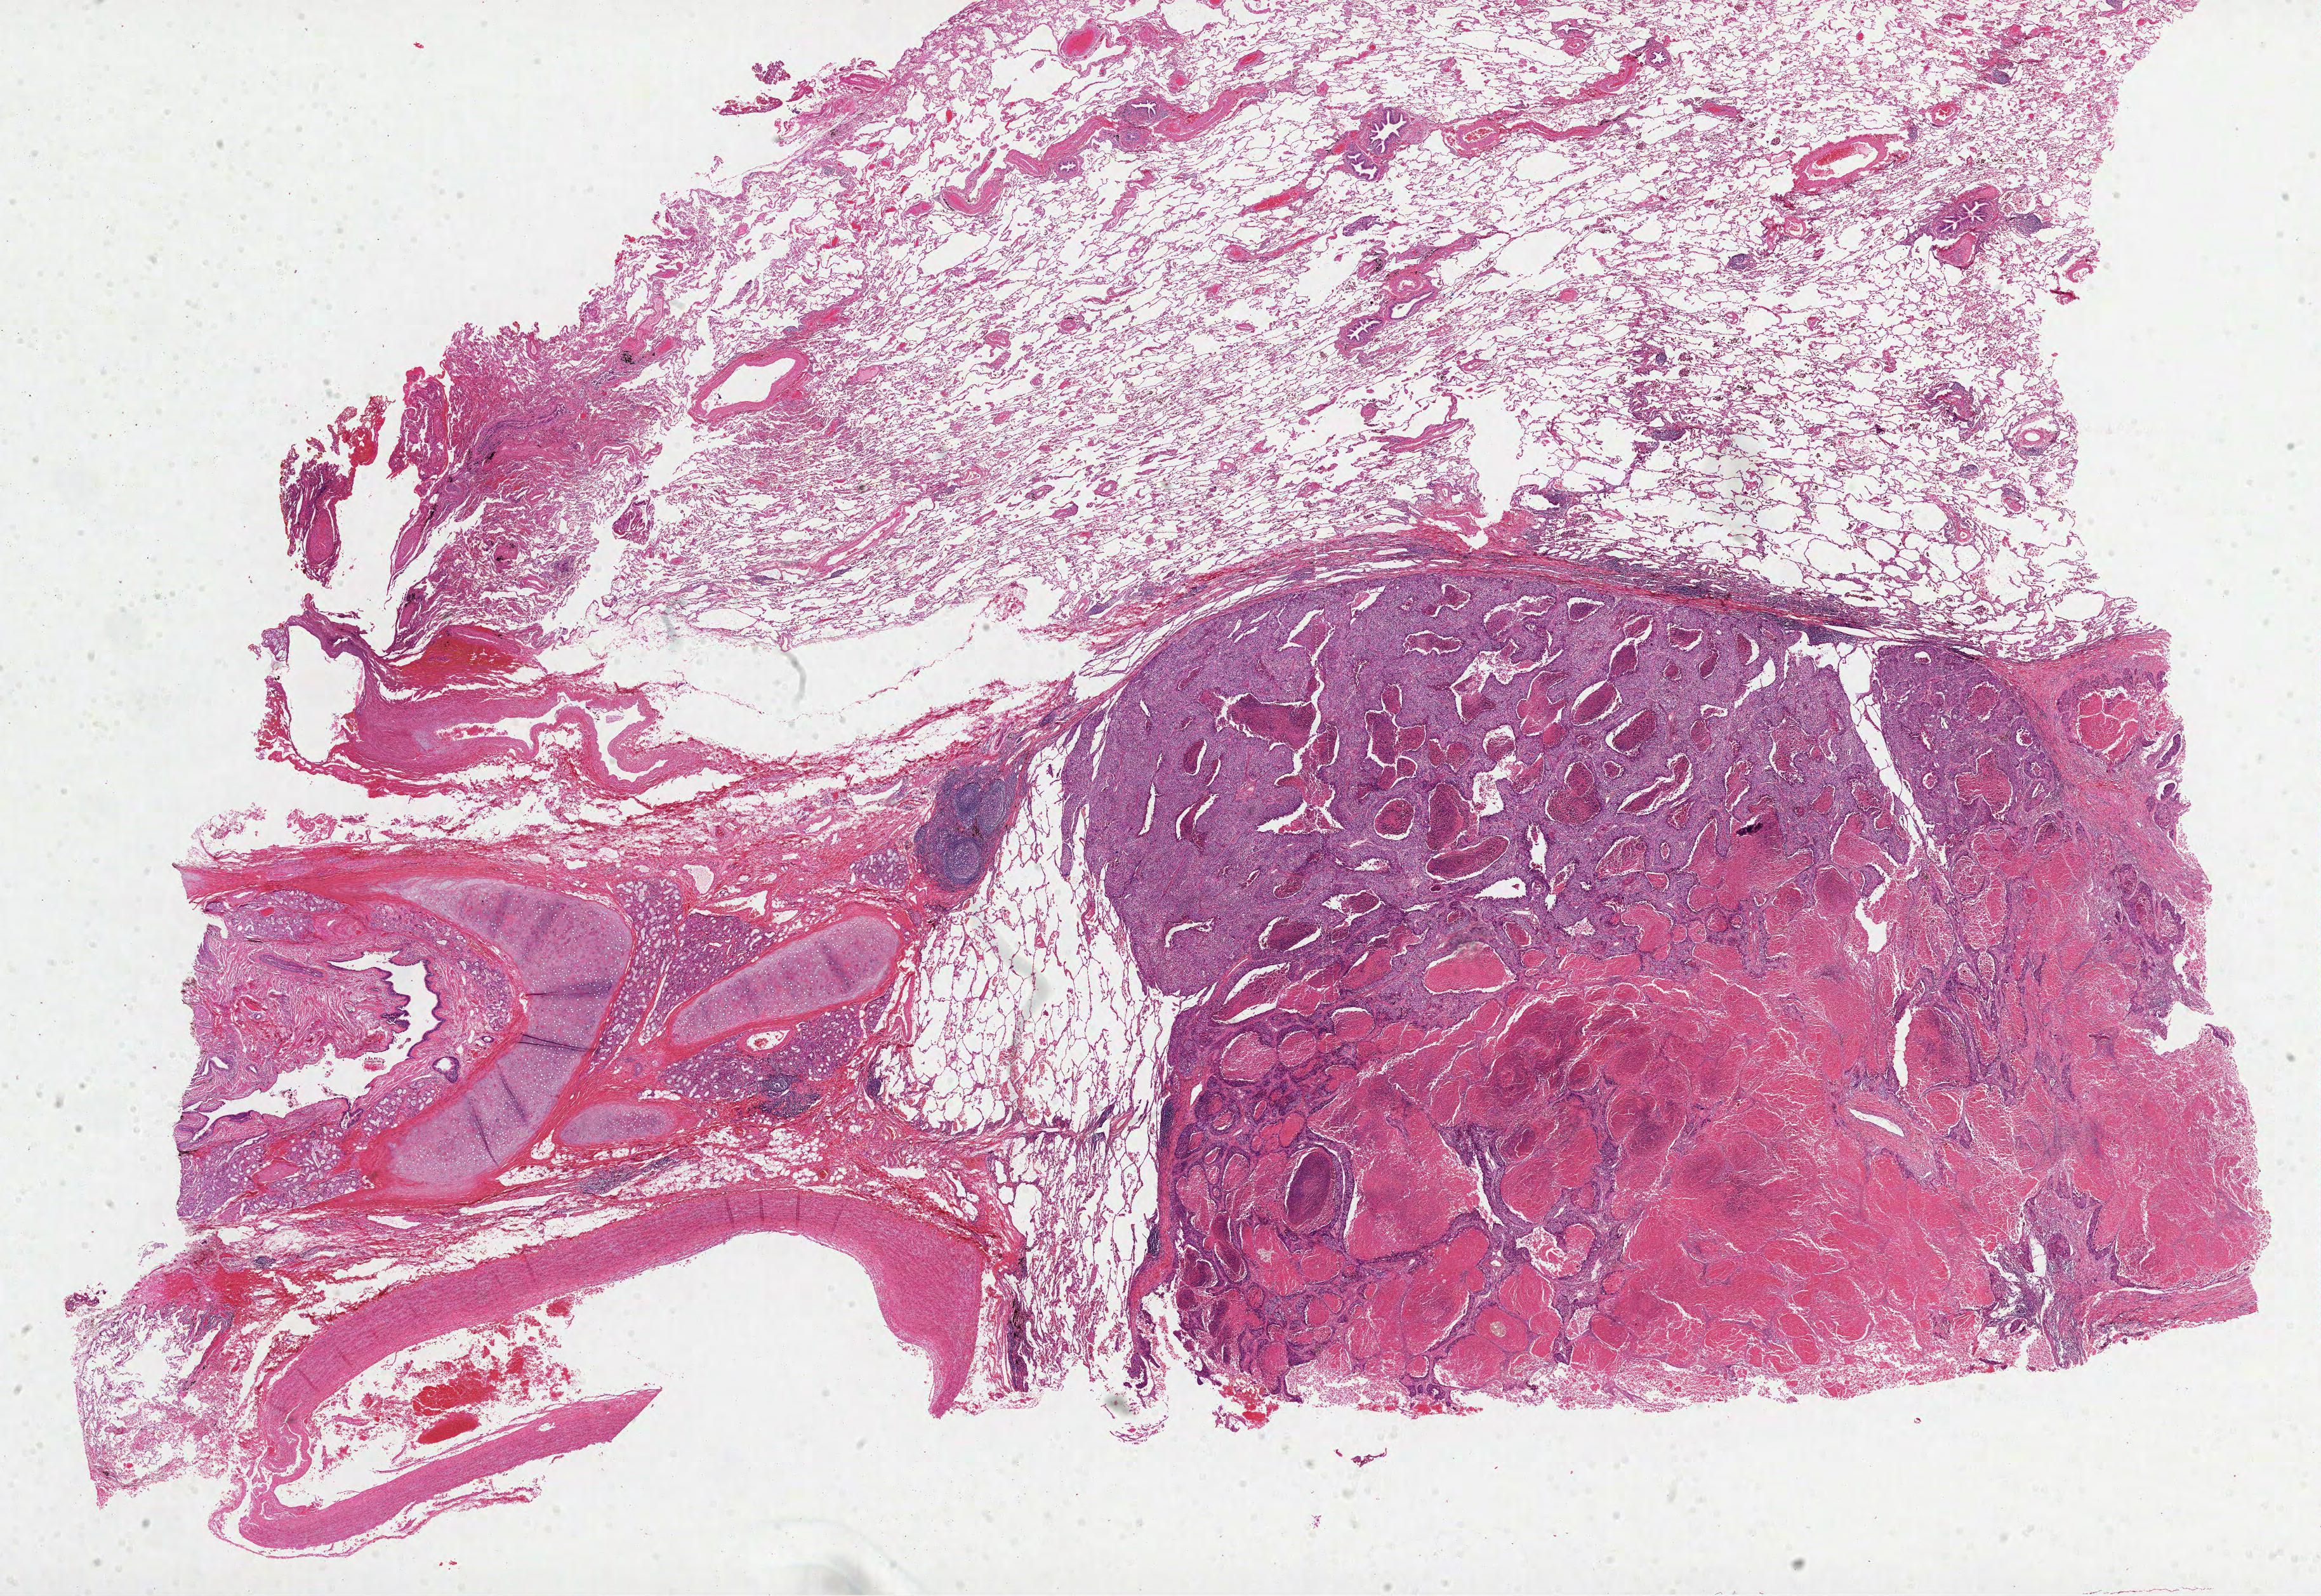
Digitized H&E tissue section (whole slide) — low-resolution overview of the scanned area, about 29.5 x 20.3 mm; formalin-fixed paraffin-embedded (FFPE) diagnostic section; lung, primary tumour sample. Male, age 69 years at initial diagnosis.
AJCC pathologic stage: IIB (6th edition). Laterality: right. Histologic diagnosis: Squamous cell carcinoma, NOS (middle lobe, lung).